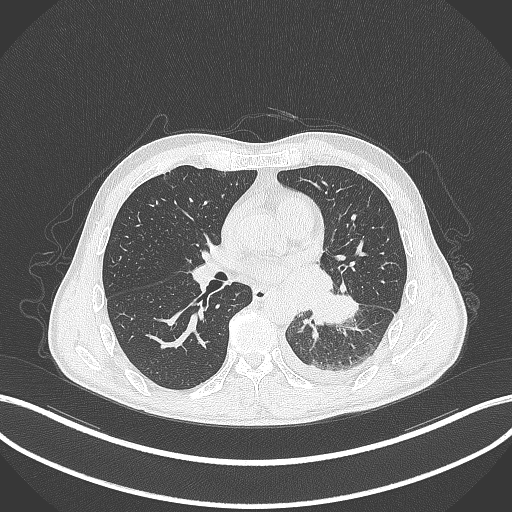
Chest CT, one axial slice. Position 158 of 295 along the scan axis. Reconstruction kernel B70f. Lung window (W 1500 / L -600 HU). 512 × 512 image matrix. Patient: male, 47 years. Case-level facts recorded for this patient, not image findings: clinical TNM (as recorded): T3 N1 M1c.
Outlined on this slice (bounding box drawn by a radiologist):
- lung tumour (recorded histology: small cell carcinoma): bounding box (x1, y1, x2, y2) in pixels: (308, 284, 361, 327)